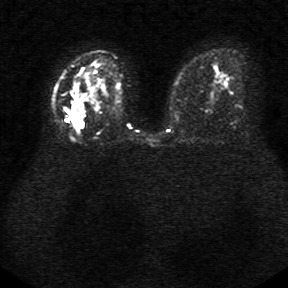
Breast MRI, one axial slice. Position 18 of 34 along the scan axis. Diffusion-weighted series; image 2 of 4 stored at this slice position (different b-values; order by instance number). 1.5 T. 5 mm slice thickness. 288 × 288 image matrix. Female patient.
Structures marked on this image (expert manual segmentation):
- tumour on diffusion-weighted imaging: bounding box [x1, y1, x2, y2] px = [75, 93, 88, 119]